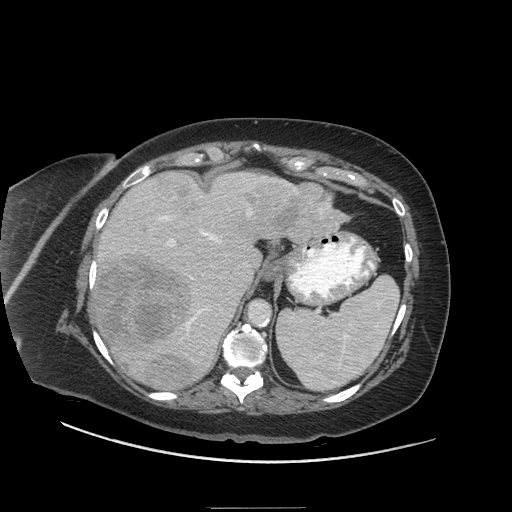
Contrast-enhanced abdominal CT (liver protocol), one axial slice; slice 44 of 81 in the series (ordered by position); 140 kVp; soft-tissue window (W 400 / L 40 HU); 512 × 512 image matrix, field of view 440 × 440 mm. Case-level facts recorded for this patient, not image findings: diagnosis: hepatocellular carcinoma (patient treated with transarterial chemoembolisation; whether this scan precedes or follows treatment is not stated here); TNM stage (as recorded): Stage-II; Child-Pugh class: A; tumour differentiation: moderately differentiated.
Annotated regions visible in this slice (semi-automatic segmentation, software-assisted and operator-edited):
- liver parenchyma outside the tumour (the mass and vessels are separate outlines, so this box may not span the whole liver): bounding box (x1, y1, x2, y2) in pixels: (90, 172, 346, 388)
- mass: (94, 173, 345, 391)
- liver vessels: (92, 176, 287, 360)